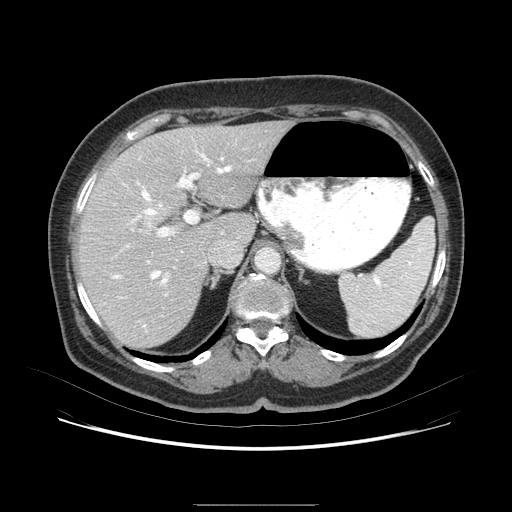
Contrast-enhanced abdominal CT (liver protocol), one axial slice; slice 51 of 79 in the series (ordered by position); 120 kVp; soft-tissue window (W 400 / L 40 HU); 2.5 mm slice thickness; 512 × 512 image matrix, field of view 380 × 380 mm. Case-level facts recorded for this patient, not image findings: diagnosis: hepatocellular carcinoma (patient treated with transarterial chemoembolisation; whether this scan precedes or follows treatment is not stated here); TNM stage (as recorded): Stage-I; Child-Pugh class: A; tumour nodularity: uninodular.
Structures marked on this image (semi-automatic segmentation, software-assisted and operator-edited):
- abdominal aorta: box from (x=256, y=248) to (x=281, y=276) px
- liver parenchyma outside the tumour (the mass and vessels are separate outlines, so this box may not span the whole liver): (x=74, y=124)–(x=296, y=346)
- liver vessels: (x=77, y=147)–(x=265, y=300)